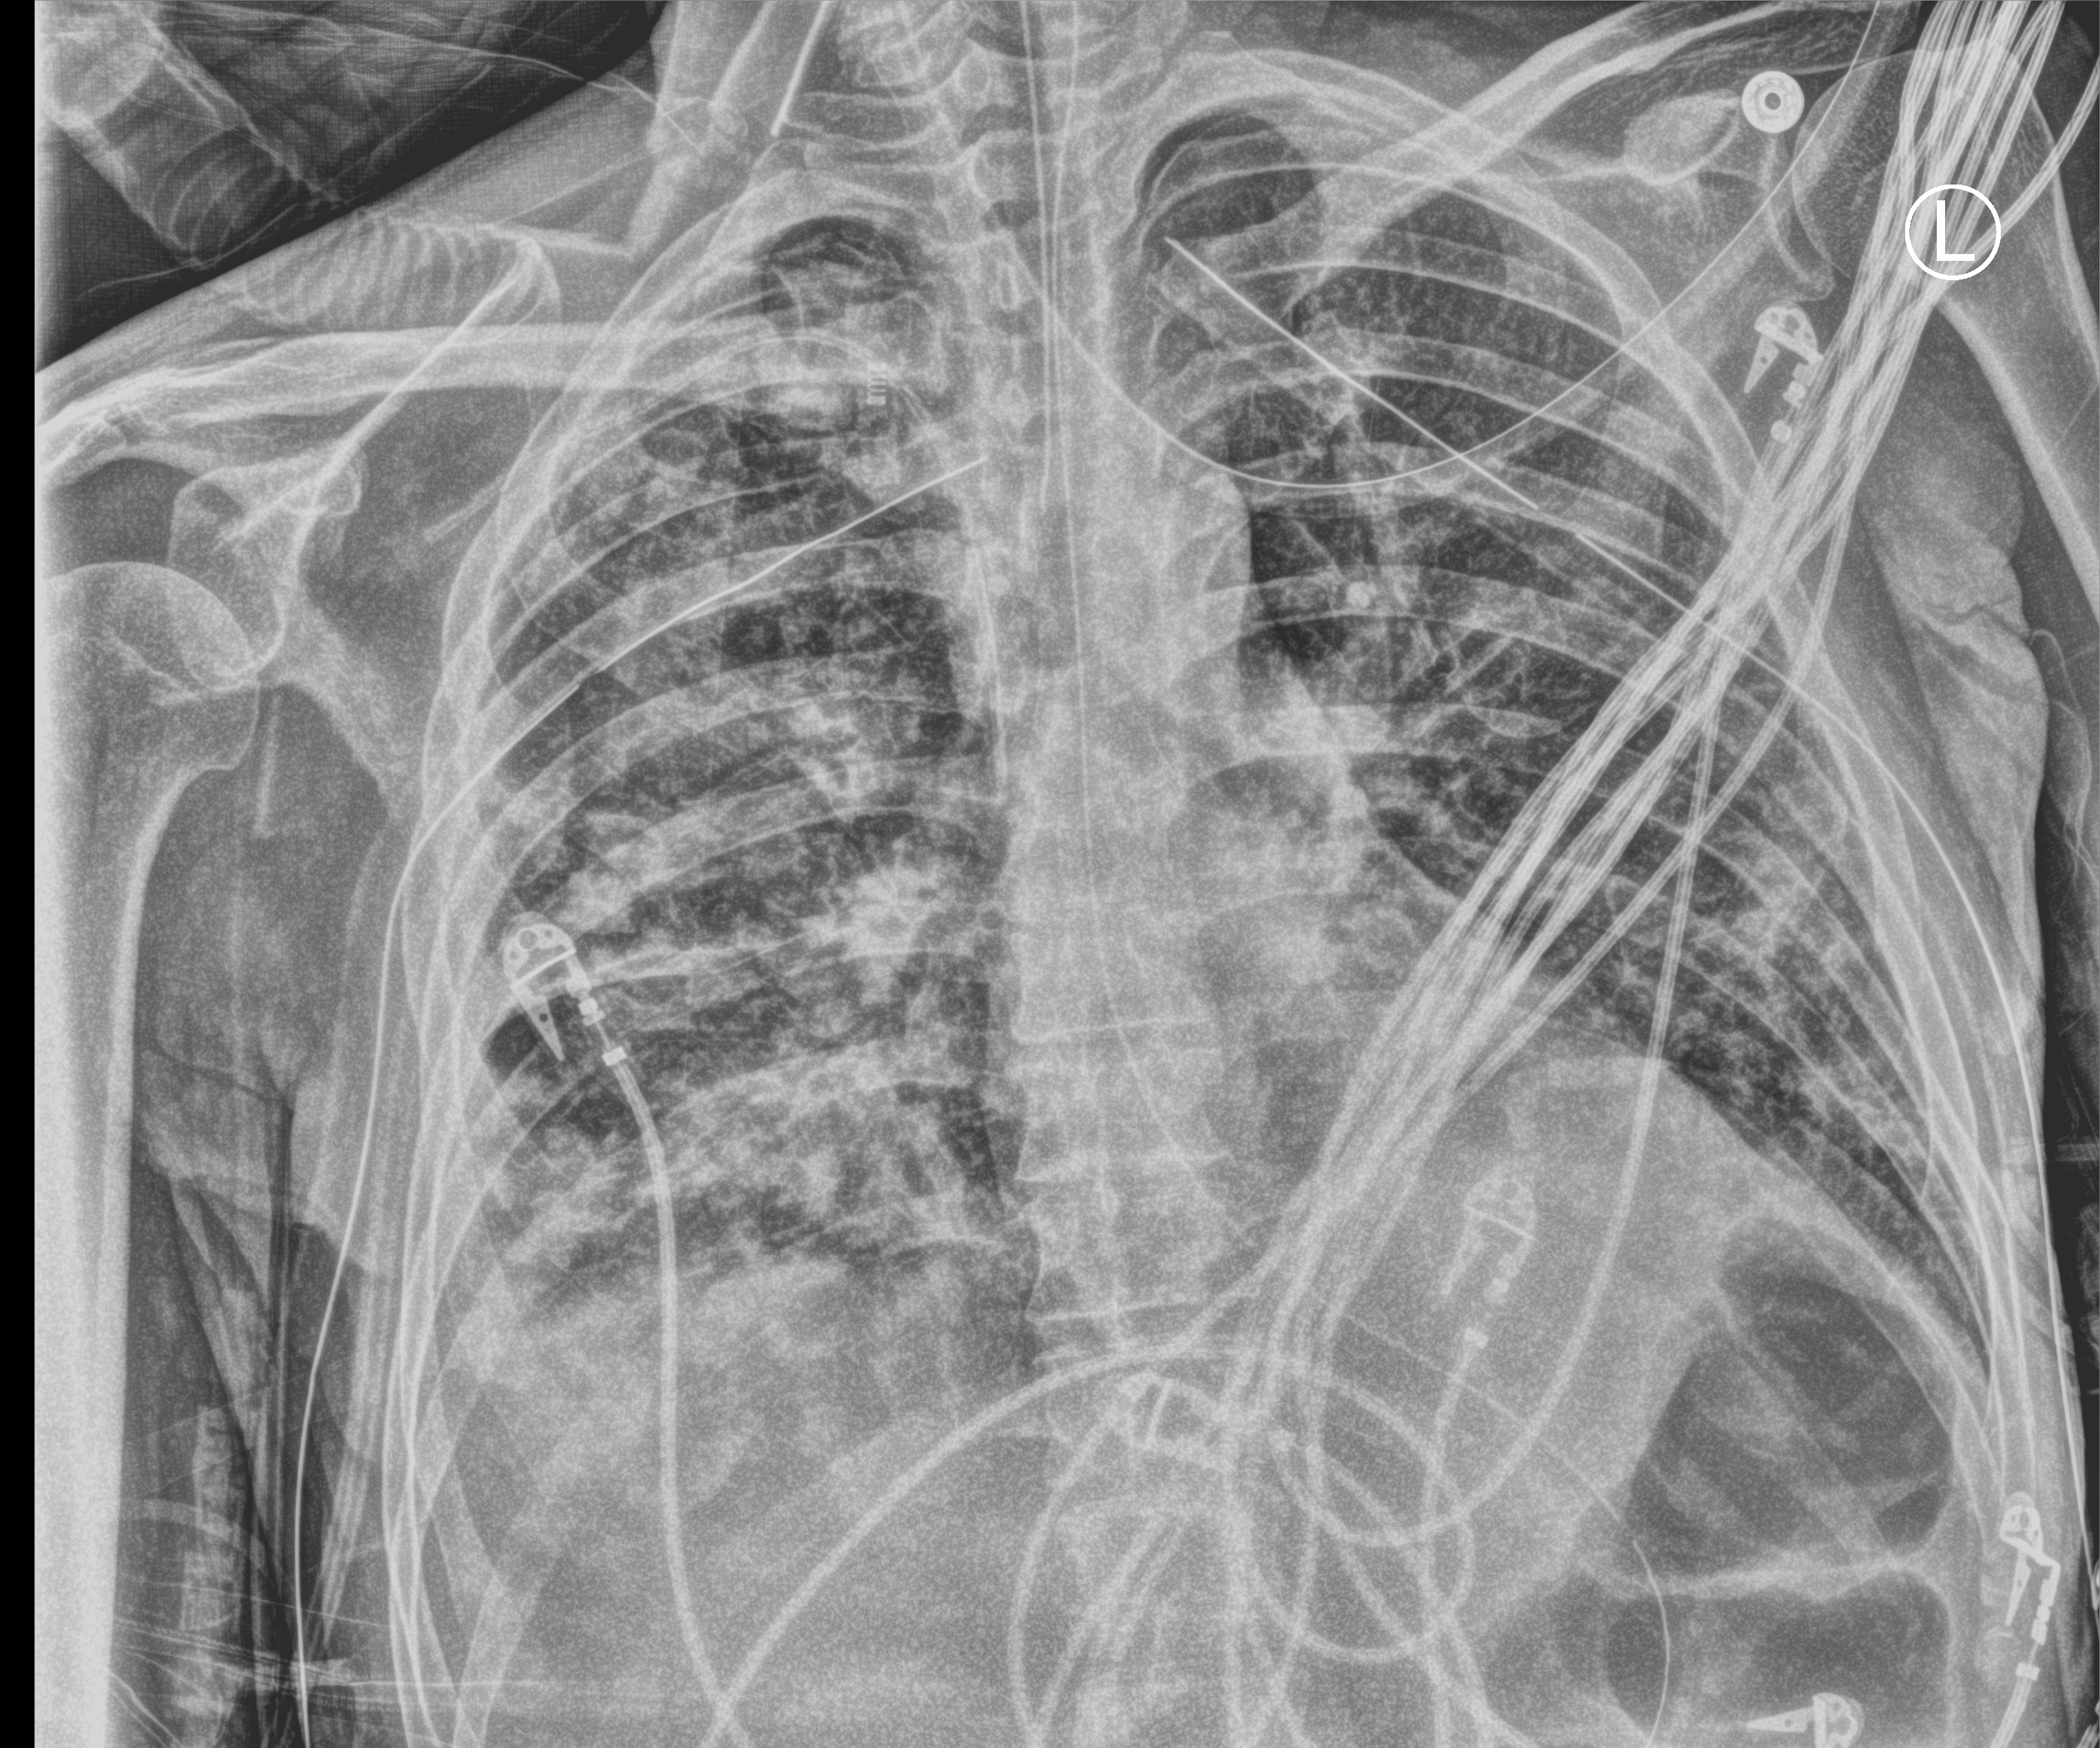
Chest X-ray (portable); anteroposterior (AP) projection. Male patient hospitalised with COVID-19, age 18–59 years.
Hospital-stay facts (about this admission, not read from this image; timing relative to this image not recorded): admitted to intensive care during this hospital stay: yes.